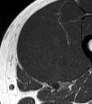
MRI of an extremity soft-tissue mass, one axial slice. Position 28 of 62 along the scan axis. MR volume resampled by the dataset authors to the PET/CT grid (not the native acquisition matrix). 3.27 mm slice thickness. 92 × 104 image matrix, field of view 90 × 102 mm. Male patient. Case-level facts recorded for this patient, not image findings: histological type: mixoid liposarcoma; grade: low; site of the primary tumour: left thigh.
Outlined on this slice (expert contour drawn on MRI and transferred to this co-registered scan by the dataset authors):
- gross tumour volume (mass): bounding box <19,22,70,82> (left, top, right, bottom; pixels)